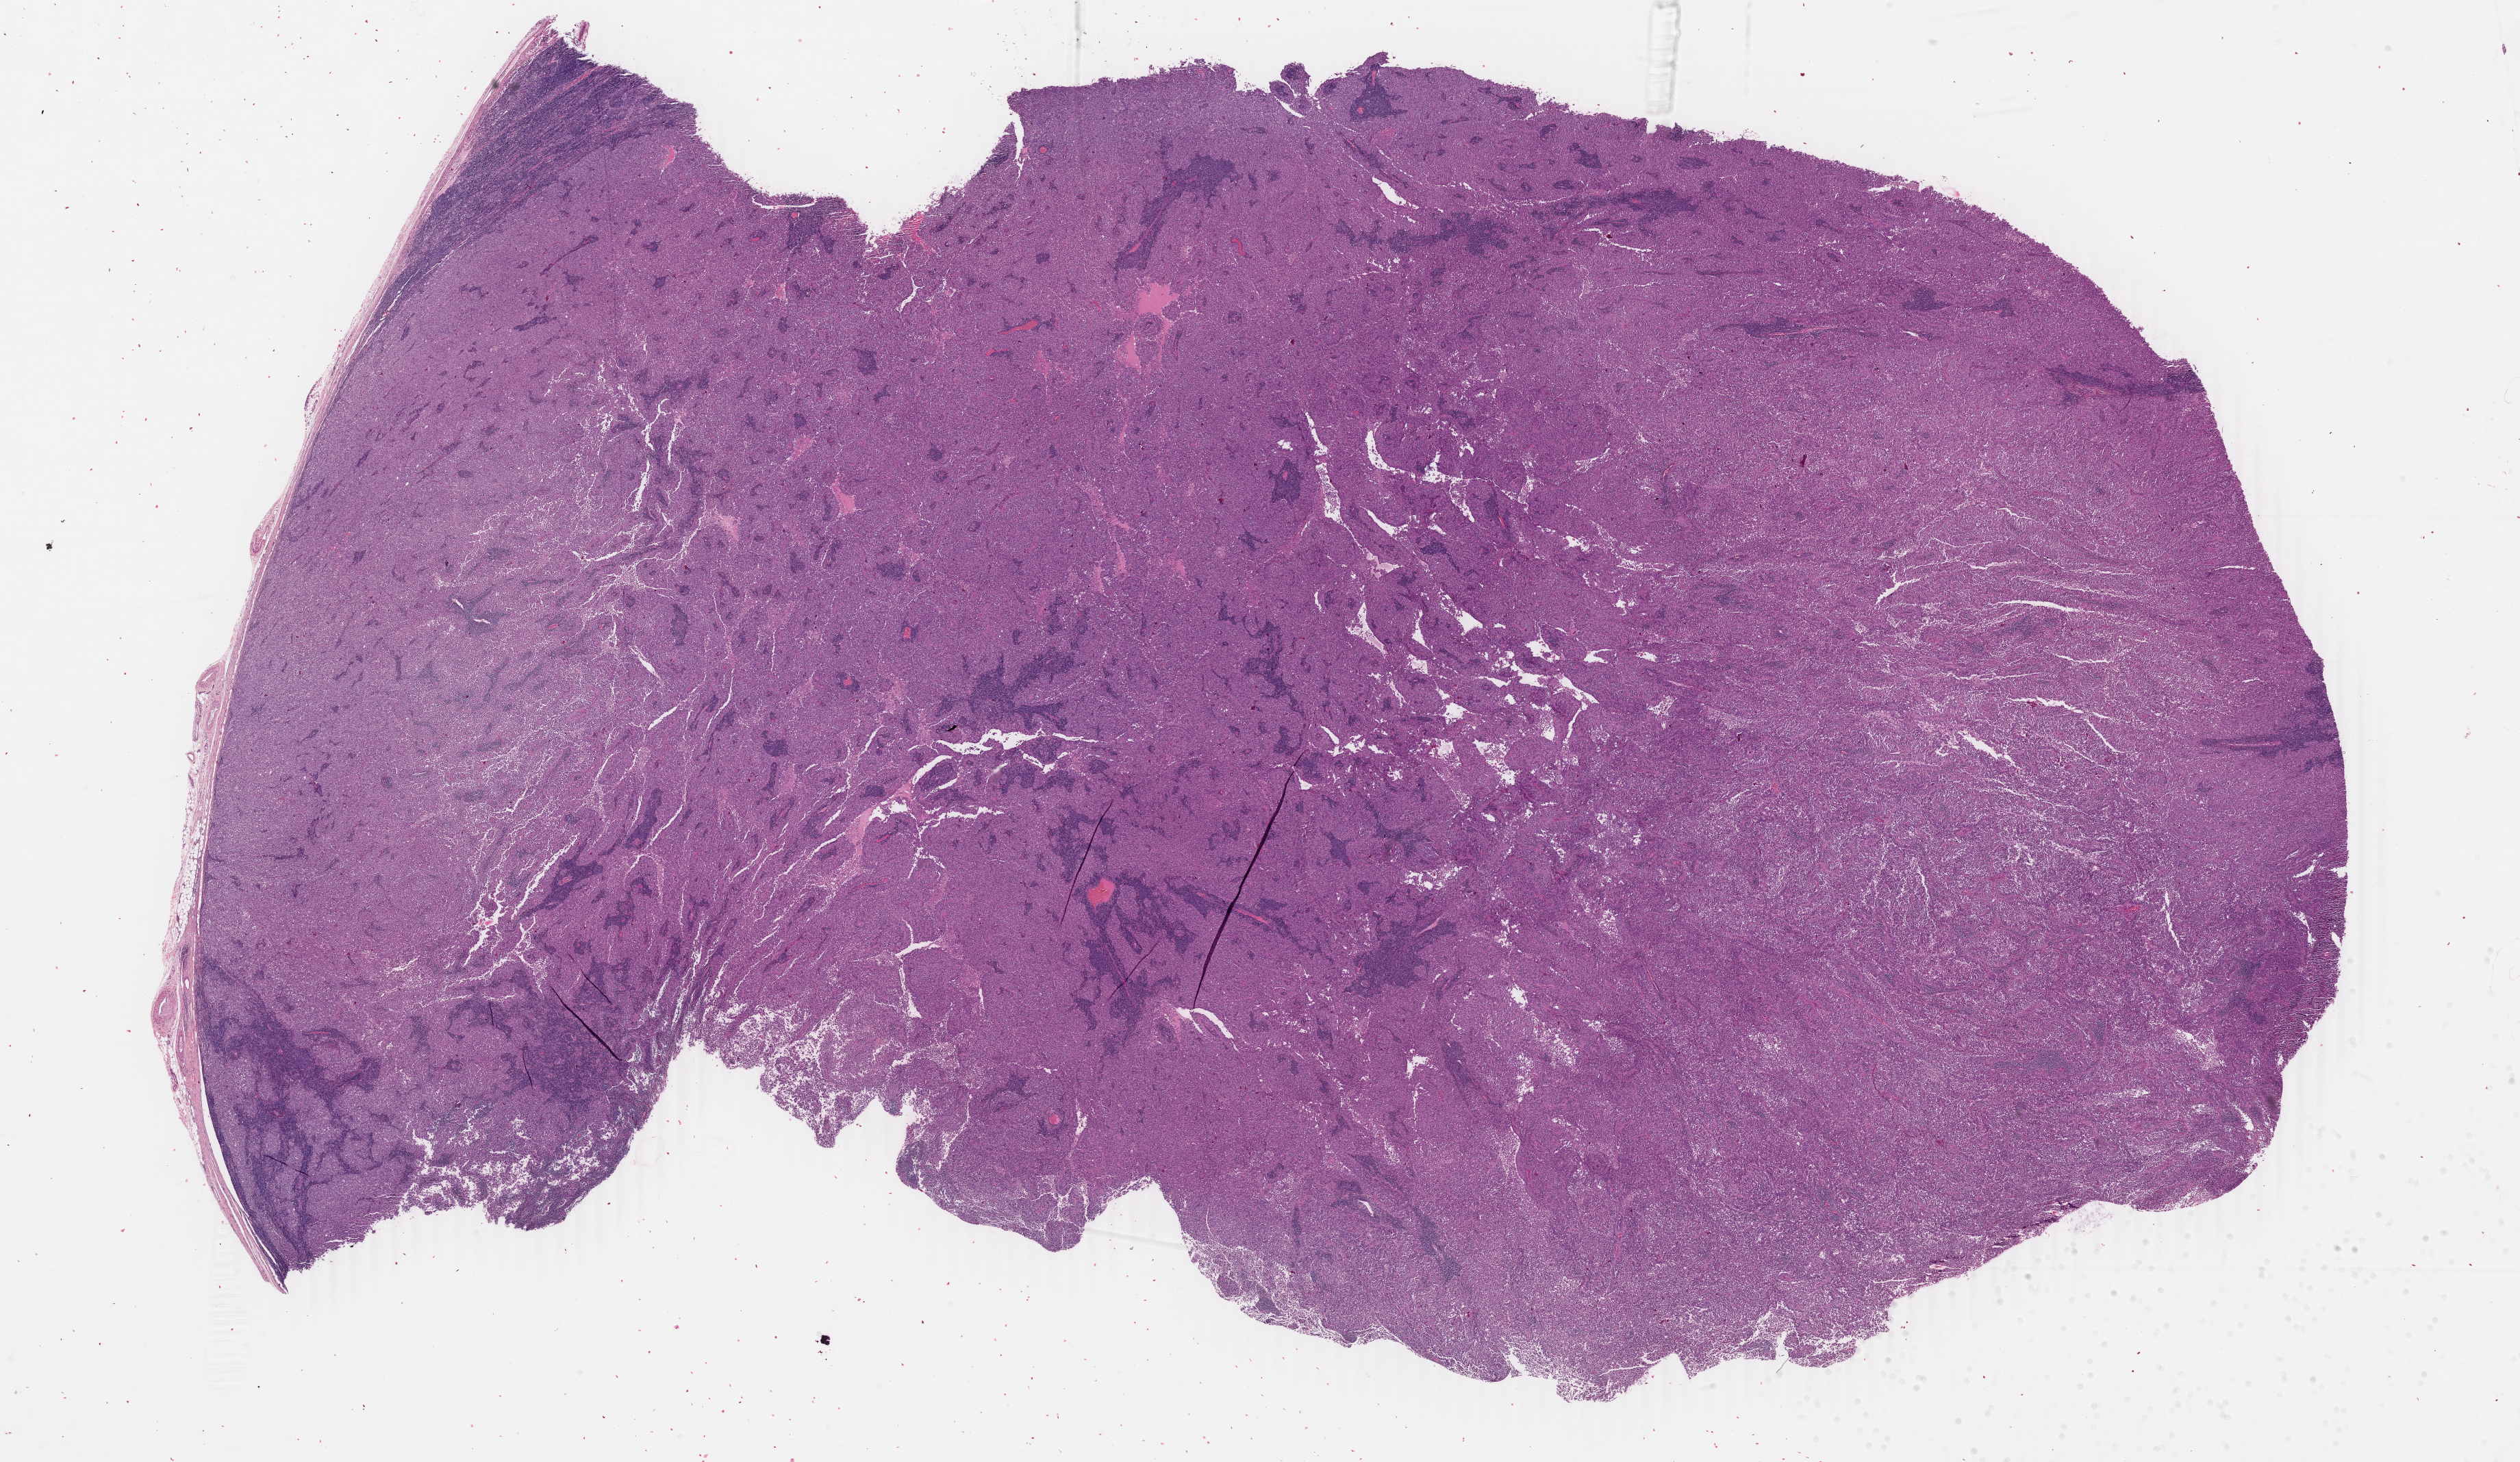
Digitized H&E-stained tissue section (whole slide) — whole scanned area (about 29.3 x 17.0 mm, slide scanned at 40x) shown as a low-resolution overview. Formalin-fixed paraffin-embedded (FFPE) diagnostic section. Skin, primary tumour sample. Patient: male, age at initial diagnosis 43 years.
• histologic diagnosis: Malignant melanoma, NOS